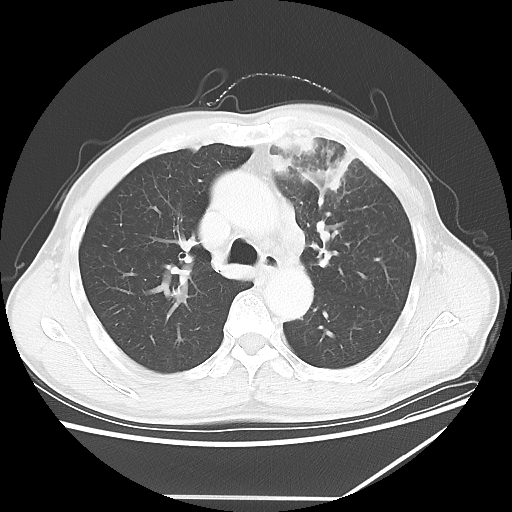
Chest CT, one axial slice. Slice 43 of 64 in the series (ordered by position). Reconstruction kernel LUNG. 100 kVp. Lung window (W 1500 / L -600 HU). 512 × 512 image matrix, field of view 383 × 383 mm. Male patient, age 64 years. From the clinical record (not read from this slice): clinical TNM (as recorded): T1c N1 M1; histopathological grade: G2.
Annotated regions visible in this slice (bounding box drawn by a radiologist):
- lung tumour (recorded histology: squamous cell carcinoma): bounding box (x1, y1, x2, y2) in pixels: (265, 126, 361, 205)